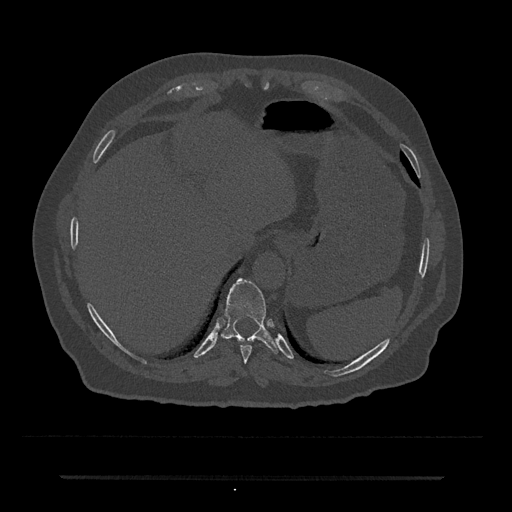
CT including the spine, one axial slice. Slice 243 of 797 in the series (ordered by position). 120 kVp. Bone window (W 1800 / L 400 HU). 512 × 512 image matrix, field of view 437 × 437 mm. Male patient, age 69 years. Case-level facts recorded for this patient, not image findings: primary cancer: prostate.
Structures marked on this image (semi-automatic segmentation, software-assisted and operator-edited):
- T10 vertebra: bounding box <222,279,279,353> (left, top, right, bottom; pixels)
- T9 vertebra: <240,345,252,364>